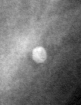
Cropped region of a digitized screen-film mammogram centred on a radiologist-marked abnormality, left breast, CC view.
Marked abnormality: calcifications, morphology round and regular; BI-RADS assessment category 2; subtlety rating 4 on a 1 (subtle) to 5 (obvious) scale; benign; no additional work-up was recommended (benign without callback).